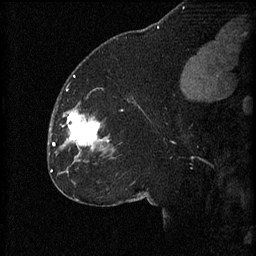
Breast MRI (dynamic contrast-enhanced), one sagittal slice; slice 29 of 60 in the series (ordered by position); 3 images stored at this slice position (order not interpretable as contrast timing); 1.5 T; TE 4.2 ms, TR 8.2 ms; 256 × 256 image matrix, field of view 180 × 180 mm. Patient: female, 32 years.
Structures marked on this image (semi-automatic segmentation, software-assisted and operator-edited):
- analysis volume of interest (the breast-tissue region the enhancement analysis was run in; not a lesion): bounding box [x1, y1, x2, y2] px = [59, 106, 111, 163]
- tumour enhancement mask (voxels above the 70 % enhancement threshold inside the analysis volume of interest): [64, 112, 109, 149]